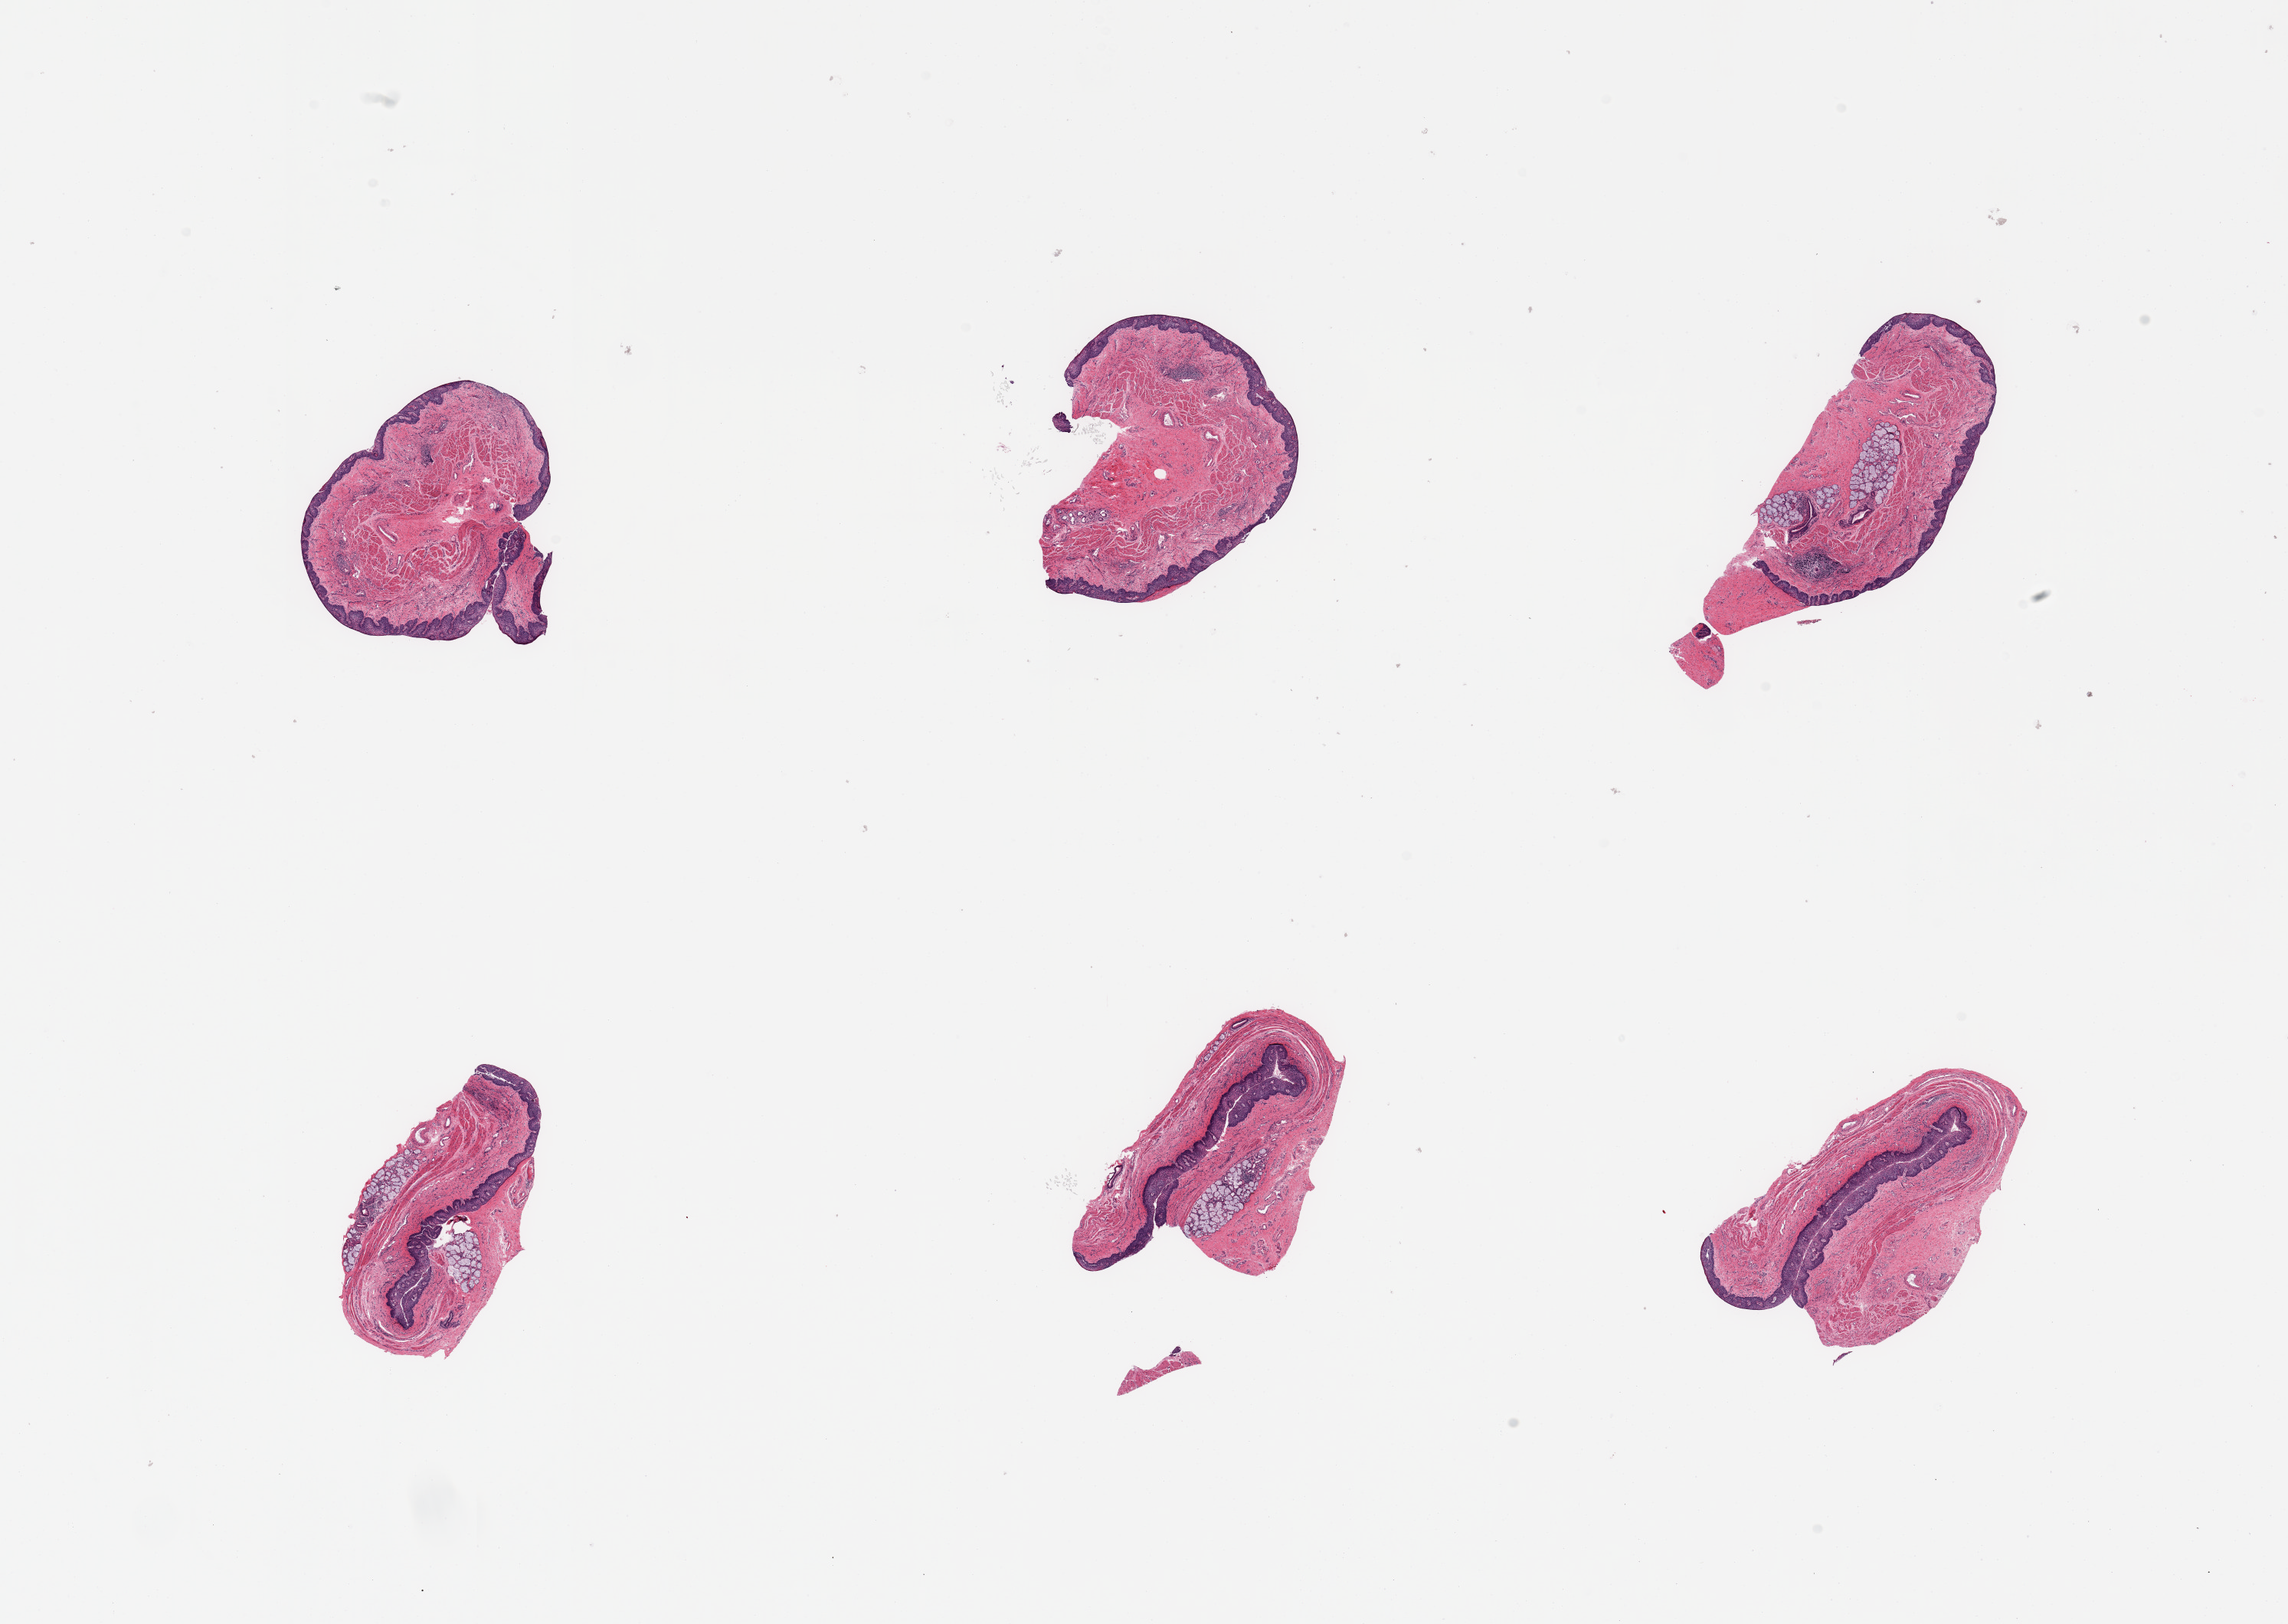
Whole-slide image, hematoxylin and eosin (H&E) stain — a low-resolution overview of the entire scanned area, about 23.6 x 16.8 mm; PAXgene-fixed, paraffin-embedded tissue; target tissue: esophageal mucous membrane; tissue donor sample. Donor: male.
Reviewer comment on this tissue sample: 6 pieces; 3 pieces have 20% submucosal gland content; foci of chronic inflammation.